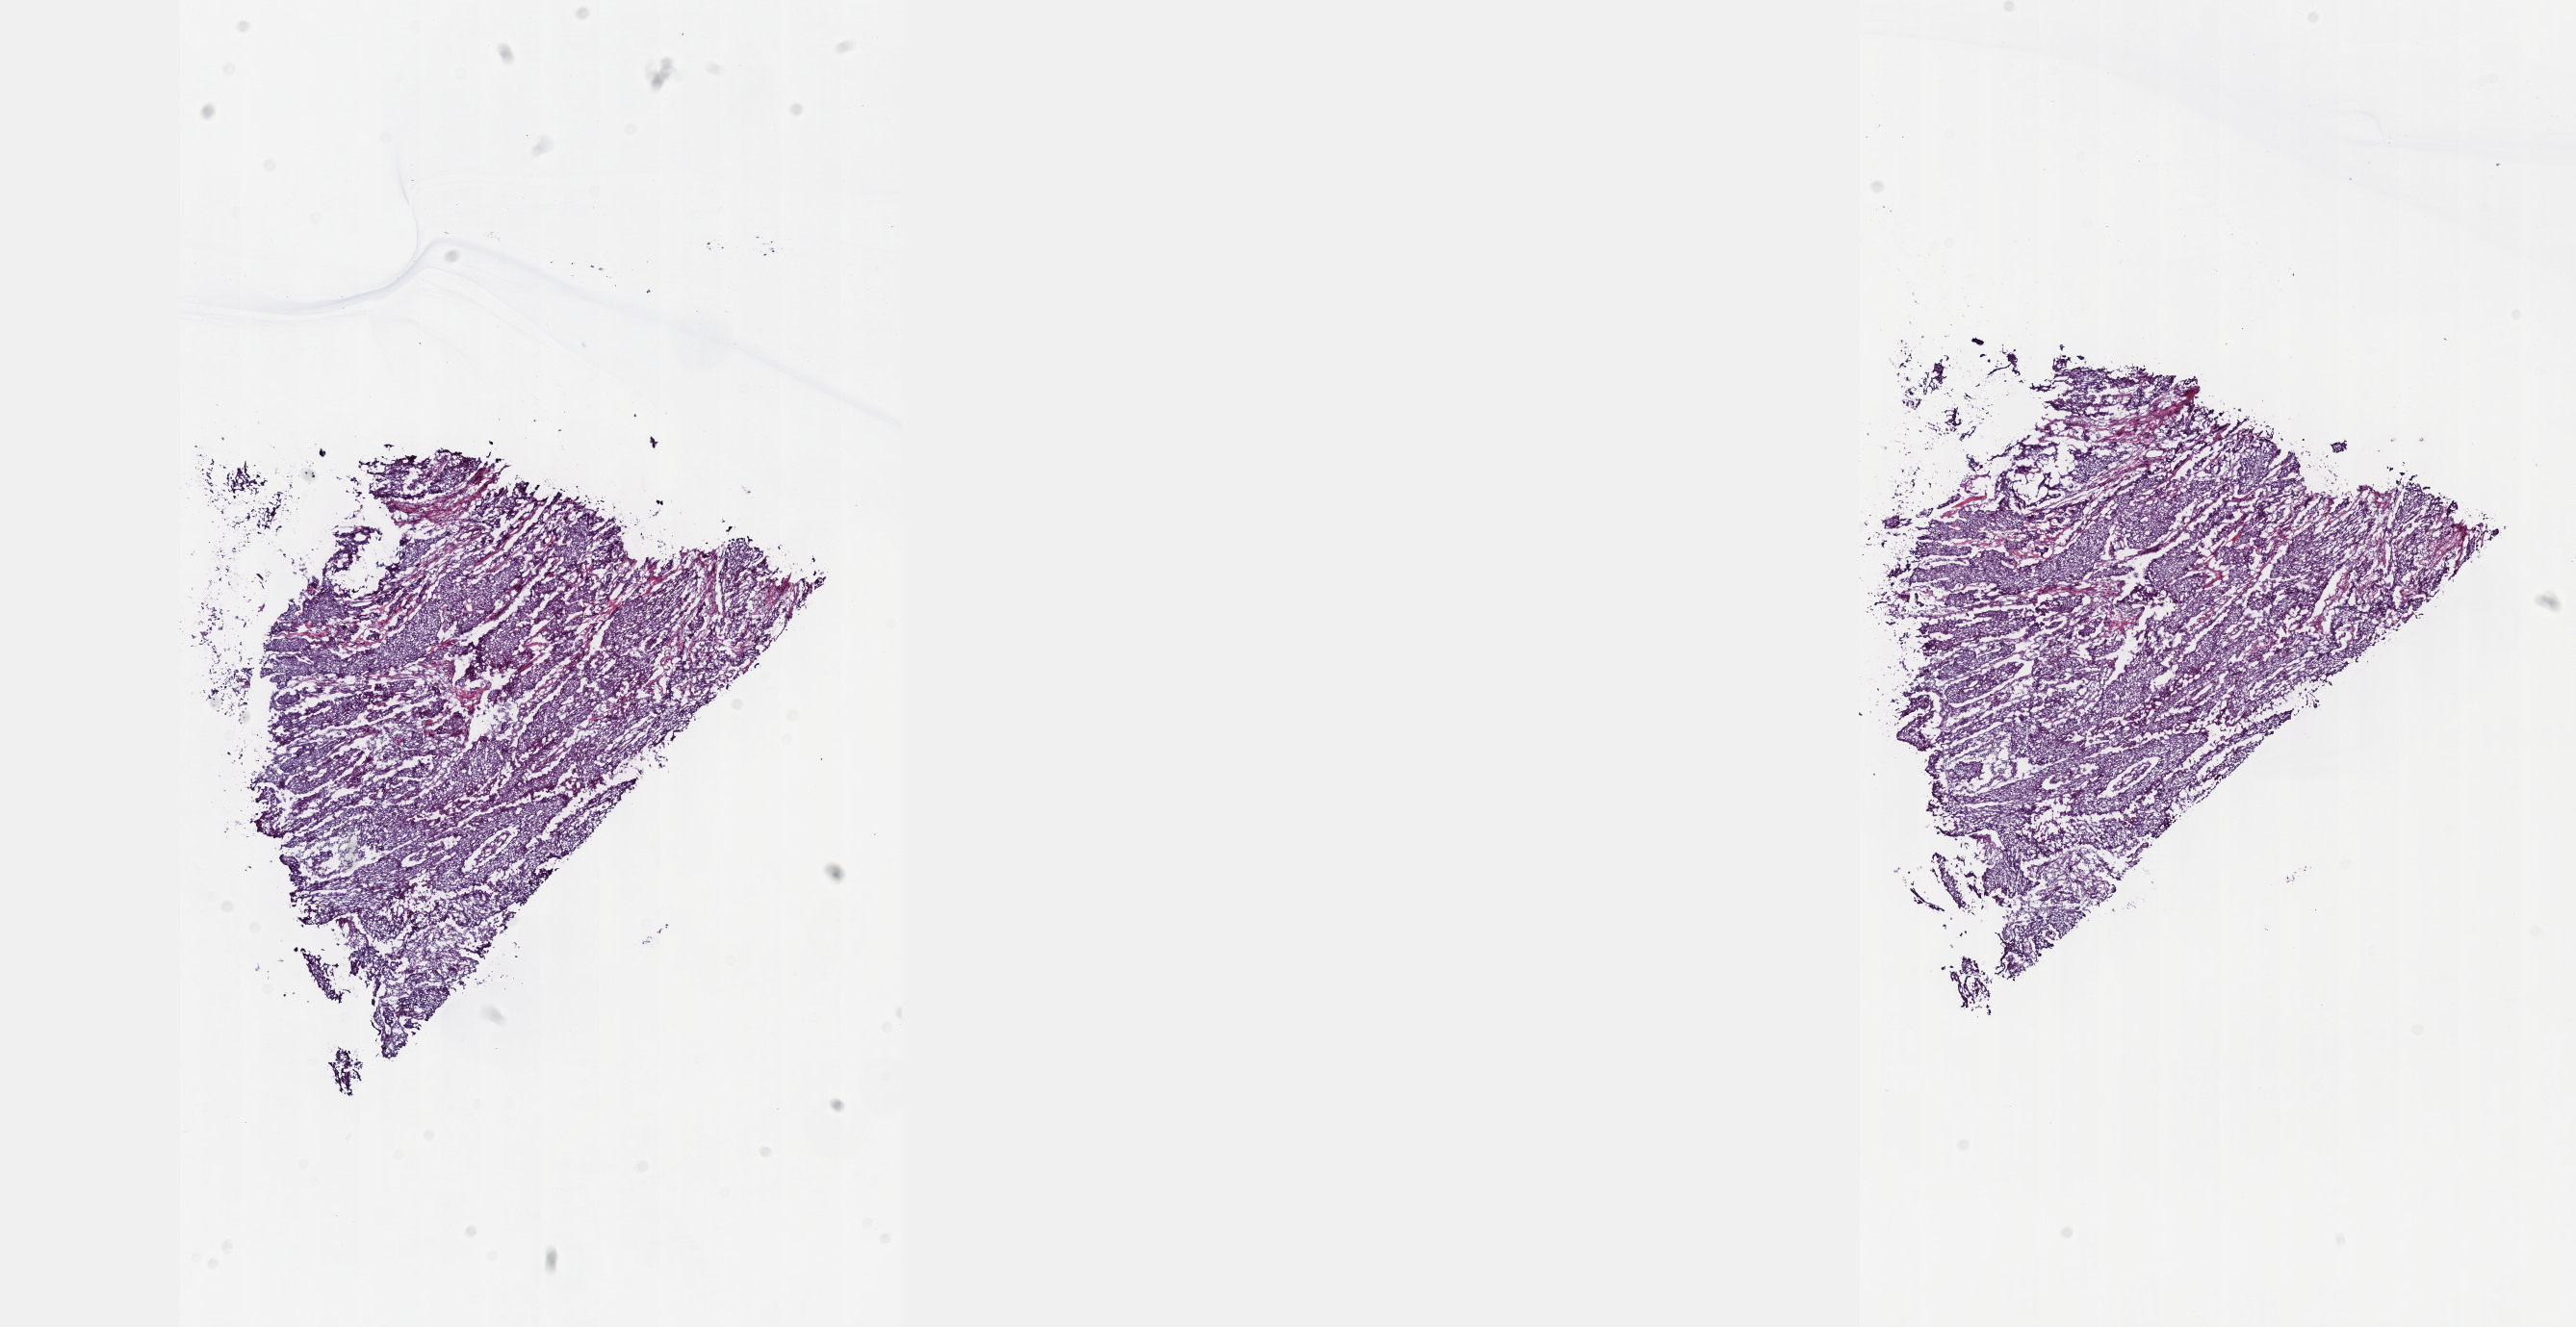
Digitized H&E-stained tissue section (whole slide), whole scanned area (about 21.6 x 11.1 mm) shown as a low-resolution overview, frozen section from the top of the tissue portion, sample: primary tumour, bladder. Patient: male, age at initial diagnosis 66 years. Histologic grade: high grade. Pathologist review of this section (percent, as recorded): tumour cells 100%, tumour nuclei 85%, normal cells 0%, stromal cells 0%, necrosis 0%. Infiltration values recorded for this section: lymphocyte infiltration 0%, monocyte infiltration 0%, neutrophil infiltration 0%.
TNM: T3b N0 M0. AJCC pathologic stage: III (6th edition). Lymph nodes positive (case pathology): 0 of 20 examined. Diagnosis: Transitional cell carcinoma.